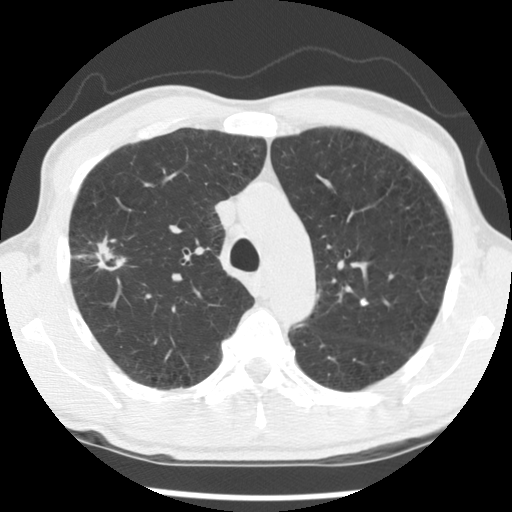
Low-dose screening chest CT, one axial slice. Position 93 of 138 along the scan axis. Reconstruction kernel STANDARD. 140 kVp. Lung window (W 1500 / L -600 HU). 2.5 mm slice thickness. 512 × 512 image matrix, field of view 320 × 320 mm.
Structures marked on this image (expert manual segmentation):
- lesion 1 (tumor, upper lobe of right lung): bounding box <72,237,126,271> (left, top, right, bottom; pixels)